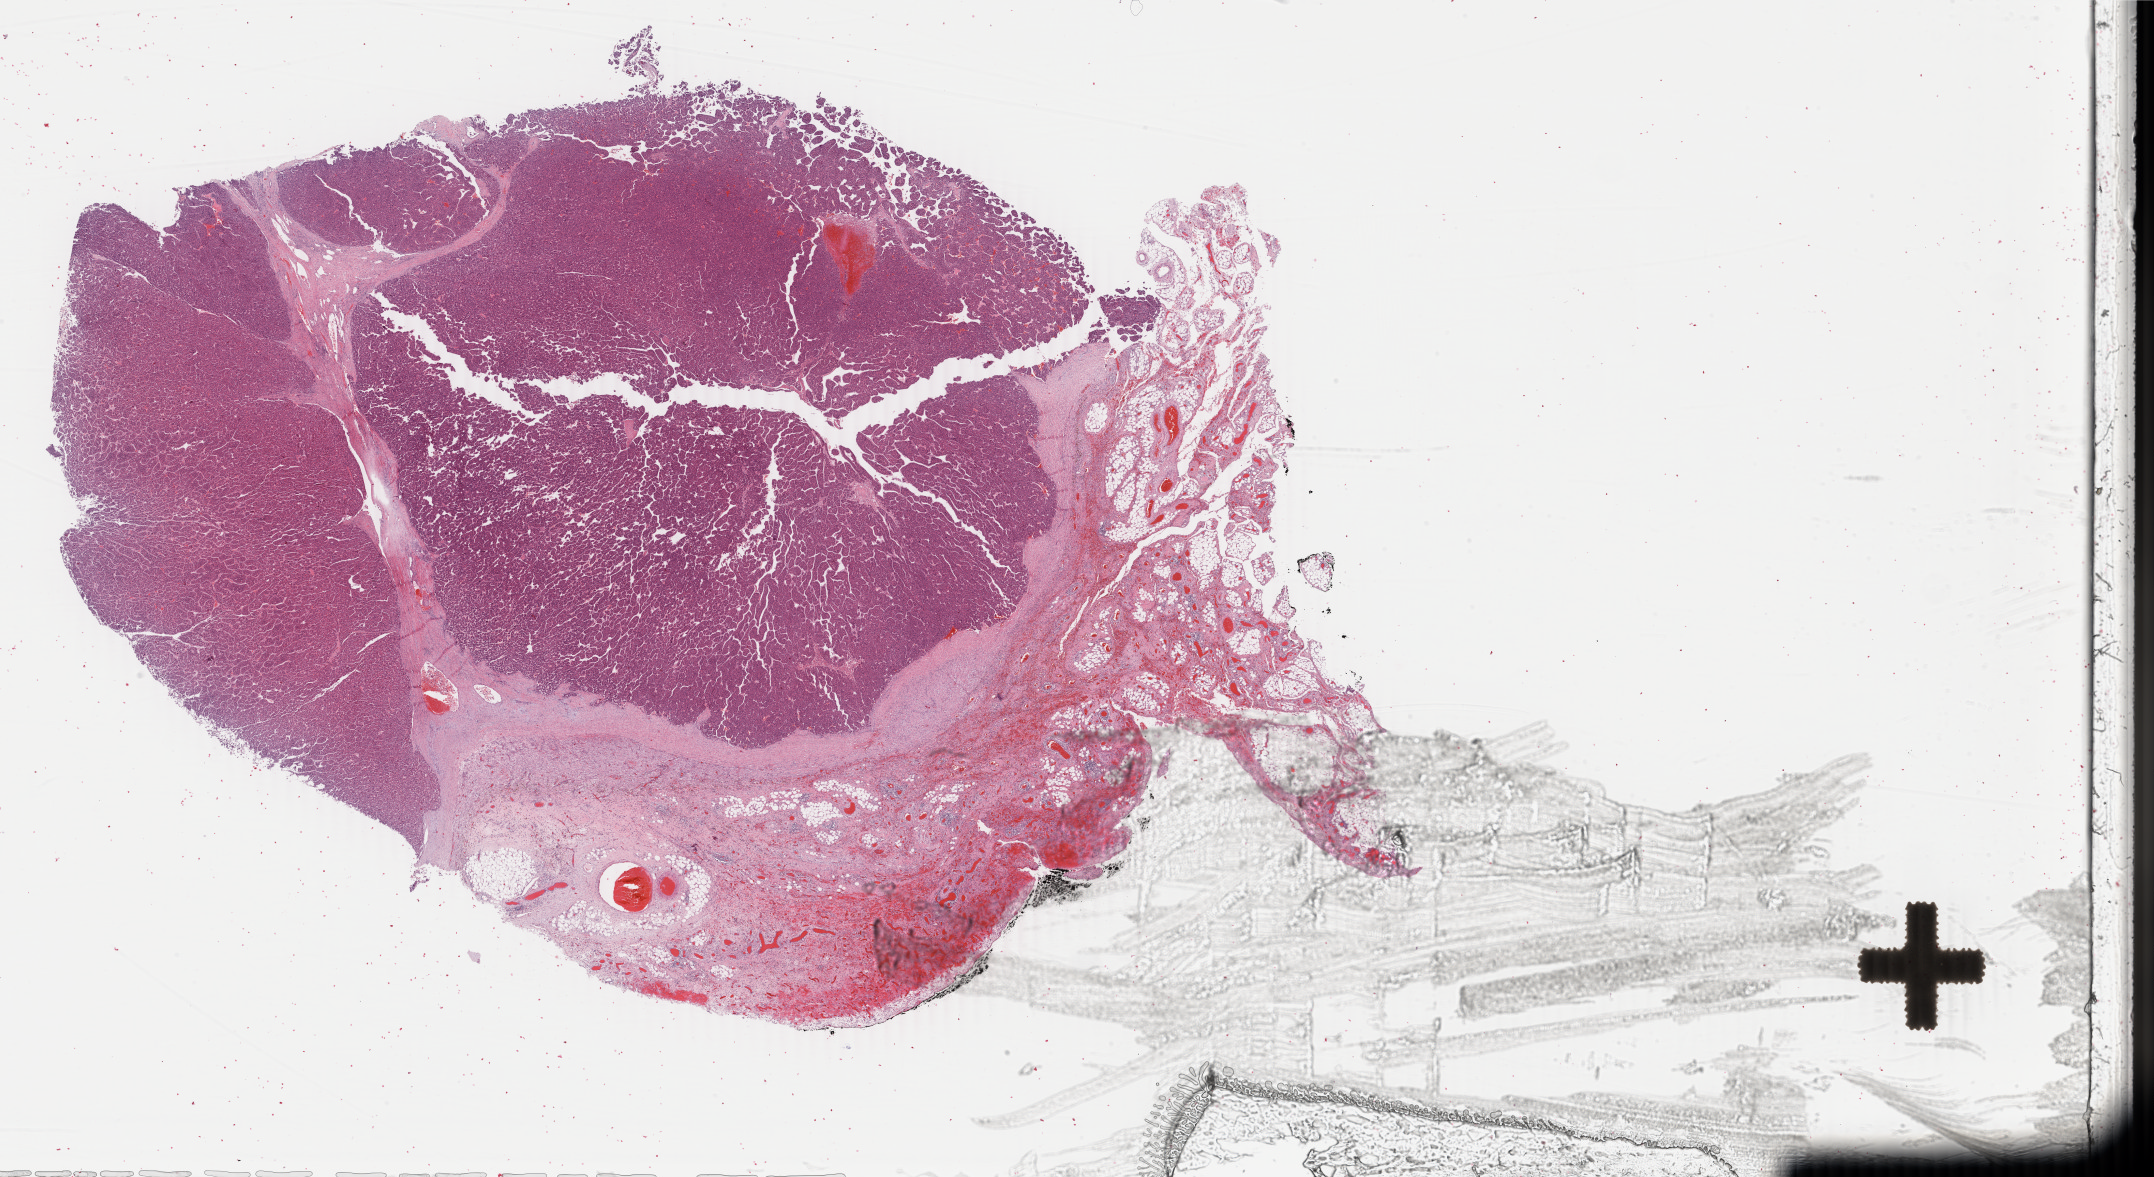
H&E whole-slide image — low-resolution overview of the scanned area, about 34.3 x 18.7 mm (from a 40x scan). Formalin-fixed paraffin-embedded (FFPE) diagnostic section. Liver, primary tumour sample. Patient: male, age at initial diagnosis 50 years. Histologic grade: G2 (moderately differentiated).
AJCC pathologic stage: IIIA. Diagnosis: Hepatocellular carcinoma, NOS.